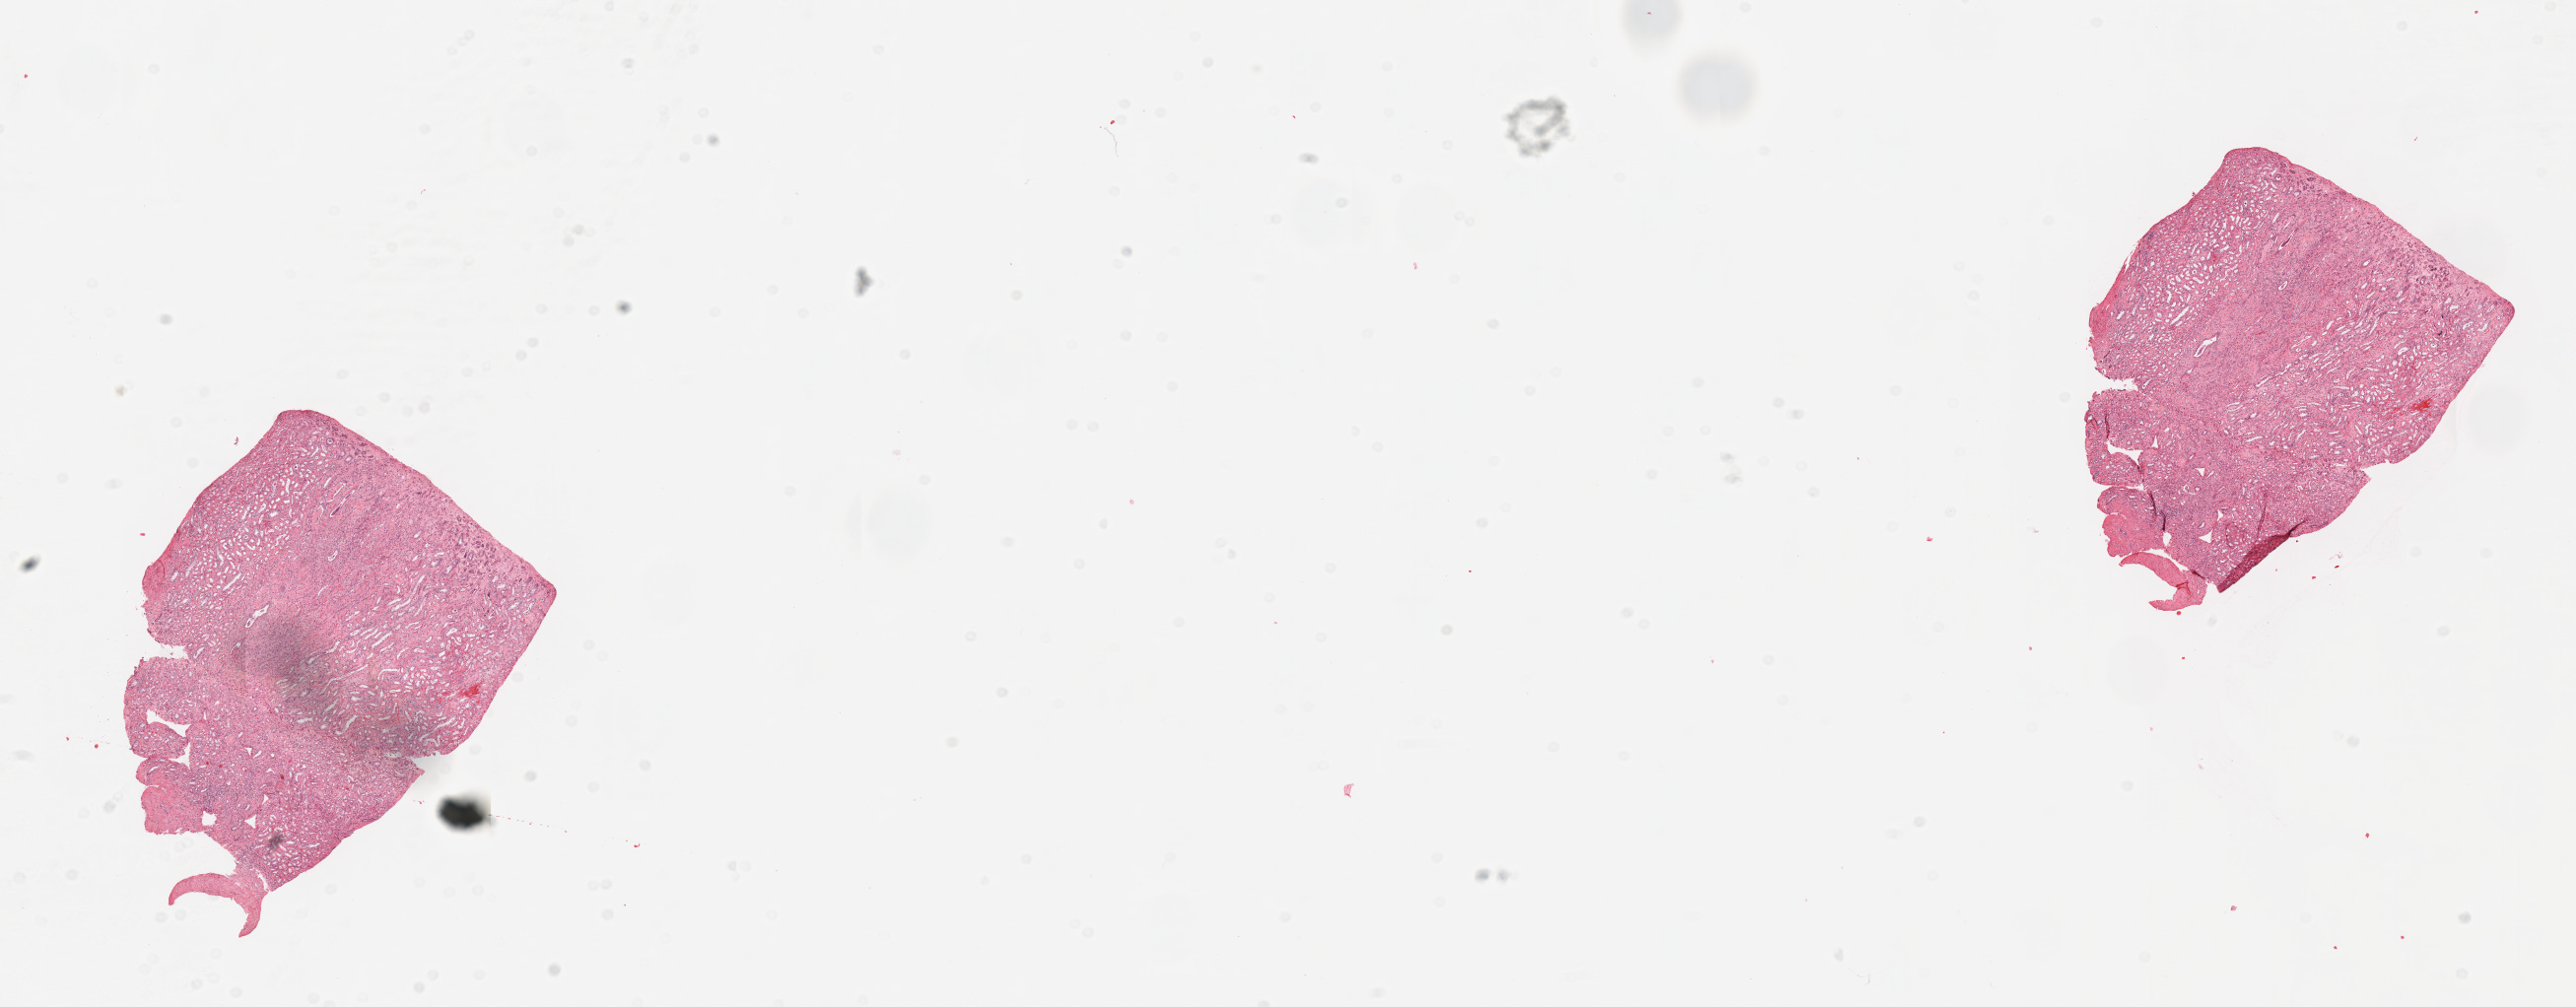
Whole-slide histology image, H&E-stained, whole scanned area (about 20.7 x 8.1 mm, from a 20x scan) shown as a low-resolution overview; normal (non-tumour) tissue sample, sampled site: kidney. 46-year-old male patient.
This section: normal (non-tumour) tissue from the same patient. Patient diagnosis: Renal cell carcinoma, NOS.